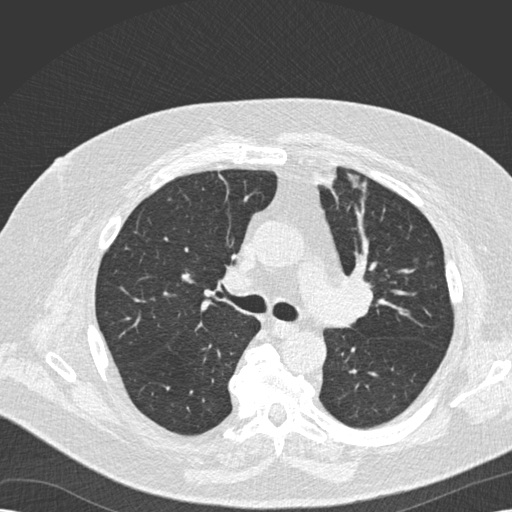
Low-dose screening chest CT, one axial slice. Position 108 of 173 along the scan axis. Reconstruction kernel B30f. 120 kVp. Lung window (W 1500 / L -600 HU). 2 mm slice thickness. 512 × 512 image matrix, field of view 370 × 370 mm.
Annotated regions visible in this slice (expert manual segmentation):
- lesion 1 (tumor, upper lobe of left lung): box from (x=319, y=165) to (x=339, y=186) px